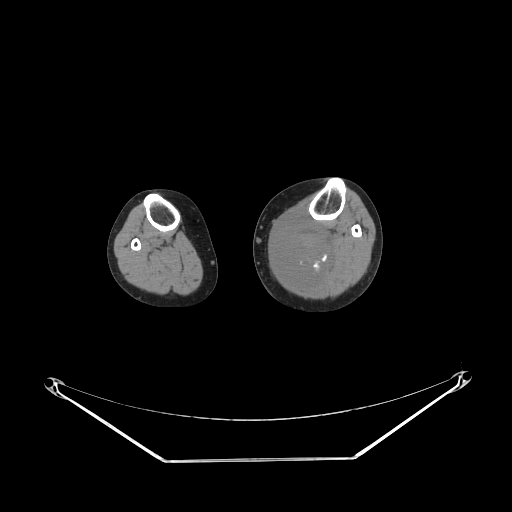
CT of an extremity soft-tissue mass (from a PET/CT study), one axial slice; reconstruction kernel STANDARD; 140 kVp; soft-tissue window (W 400 / L 40 HU); 3.75 mm slice thickness; 512 × 512 image matrix, field of view 500 × 500 mm. Female patient. From the clinical record (not read from this slice): histological type: extraskeletal high grade osteogenic sarcoma; grade: high; site of the primary tumour: left calf.
Outlined on this slice (expert contour drawn on MRI and transferred to this co-registered scan by the dataset authors):
- gross tumour volume (mass): bounding box <272,217,334,284> (left, top, right, bottom; pixels)